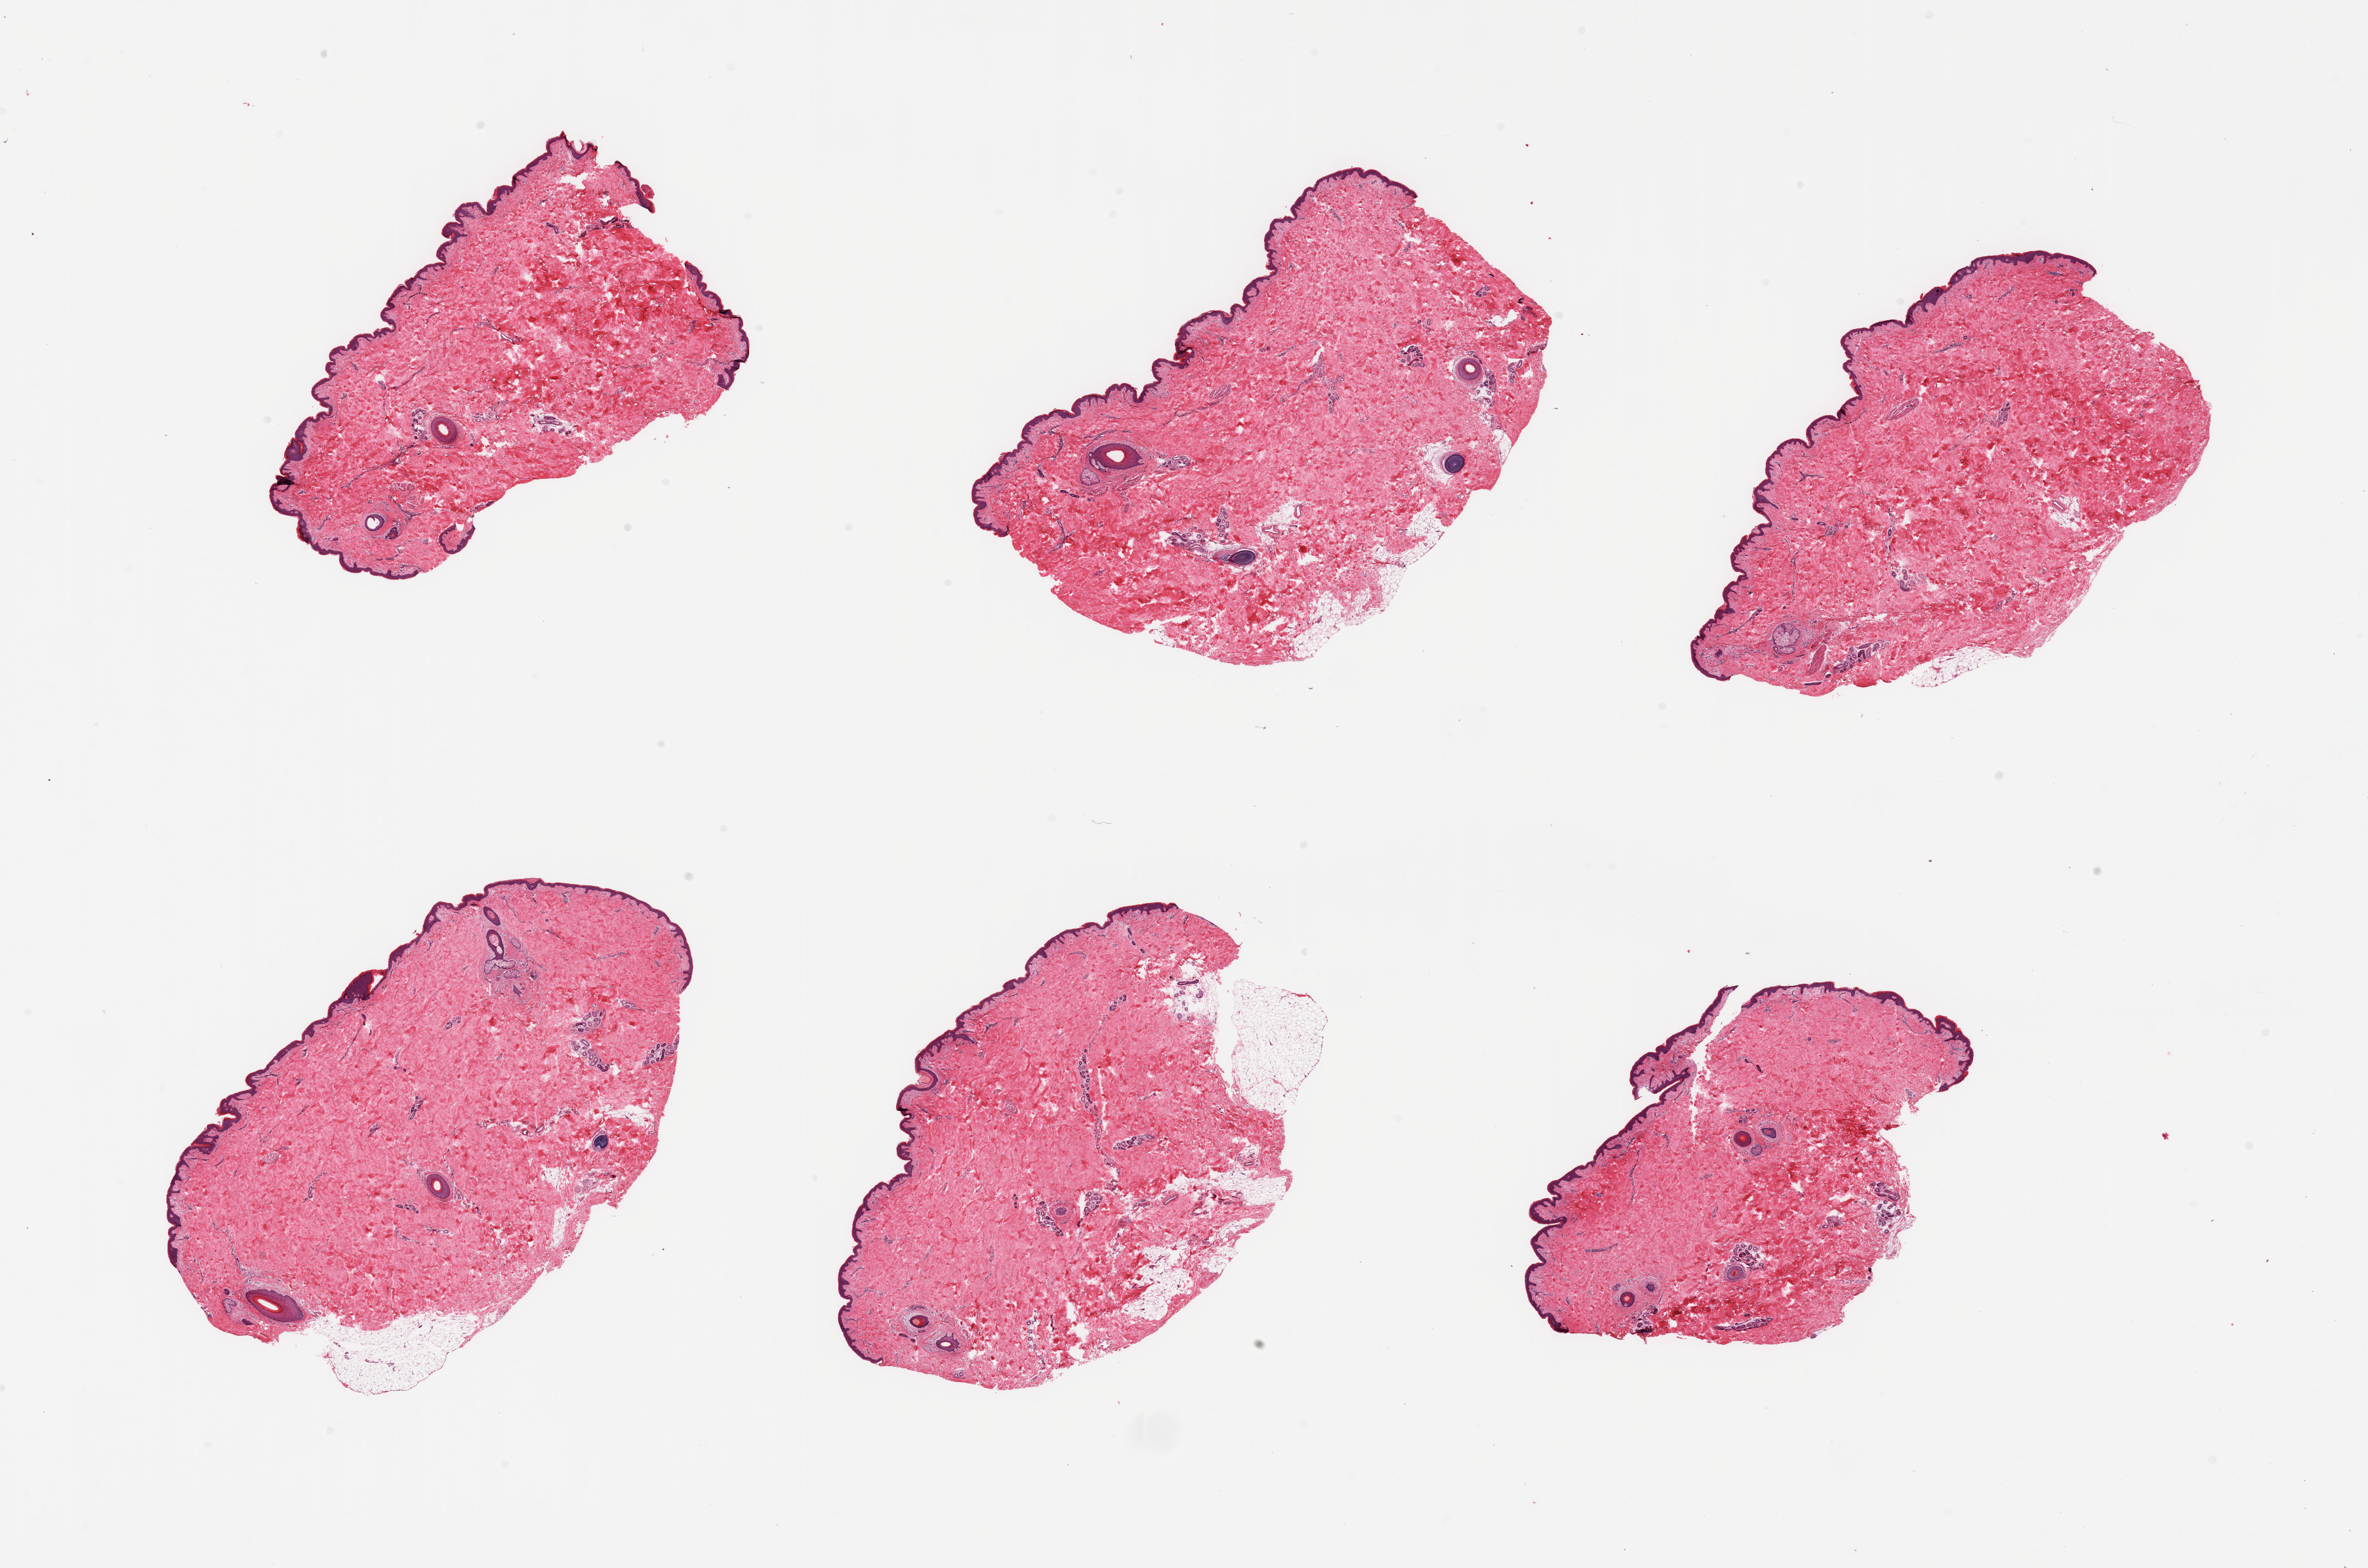
Whole-slide image, hematoxylin and eosin (H&E) stain — whole scanned area (about 28.5 x 18.9 mm) shown as a low-resolution overview. PAXgene-fixed paraffin-embedded (PFPE) section. Target tissue: skin of suprapubic region. Donor tissue sample. Donor sex: male.
• reviewer comment on this tissue sample: 6 pieces, minimal dermal fat; squamous epithelium is ~ 40 microns